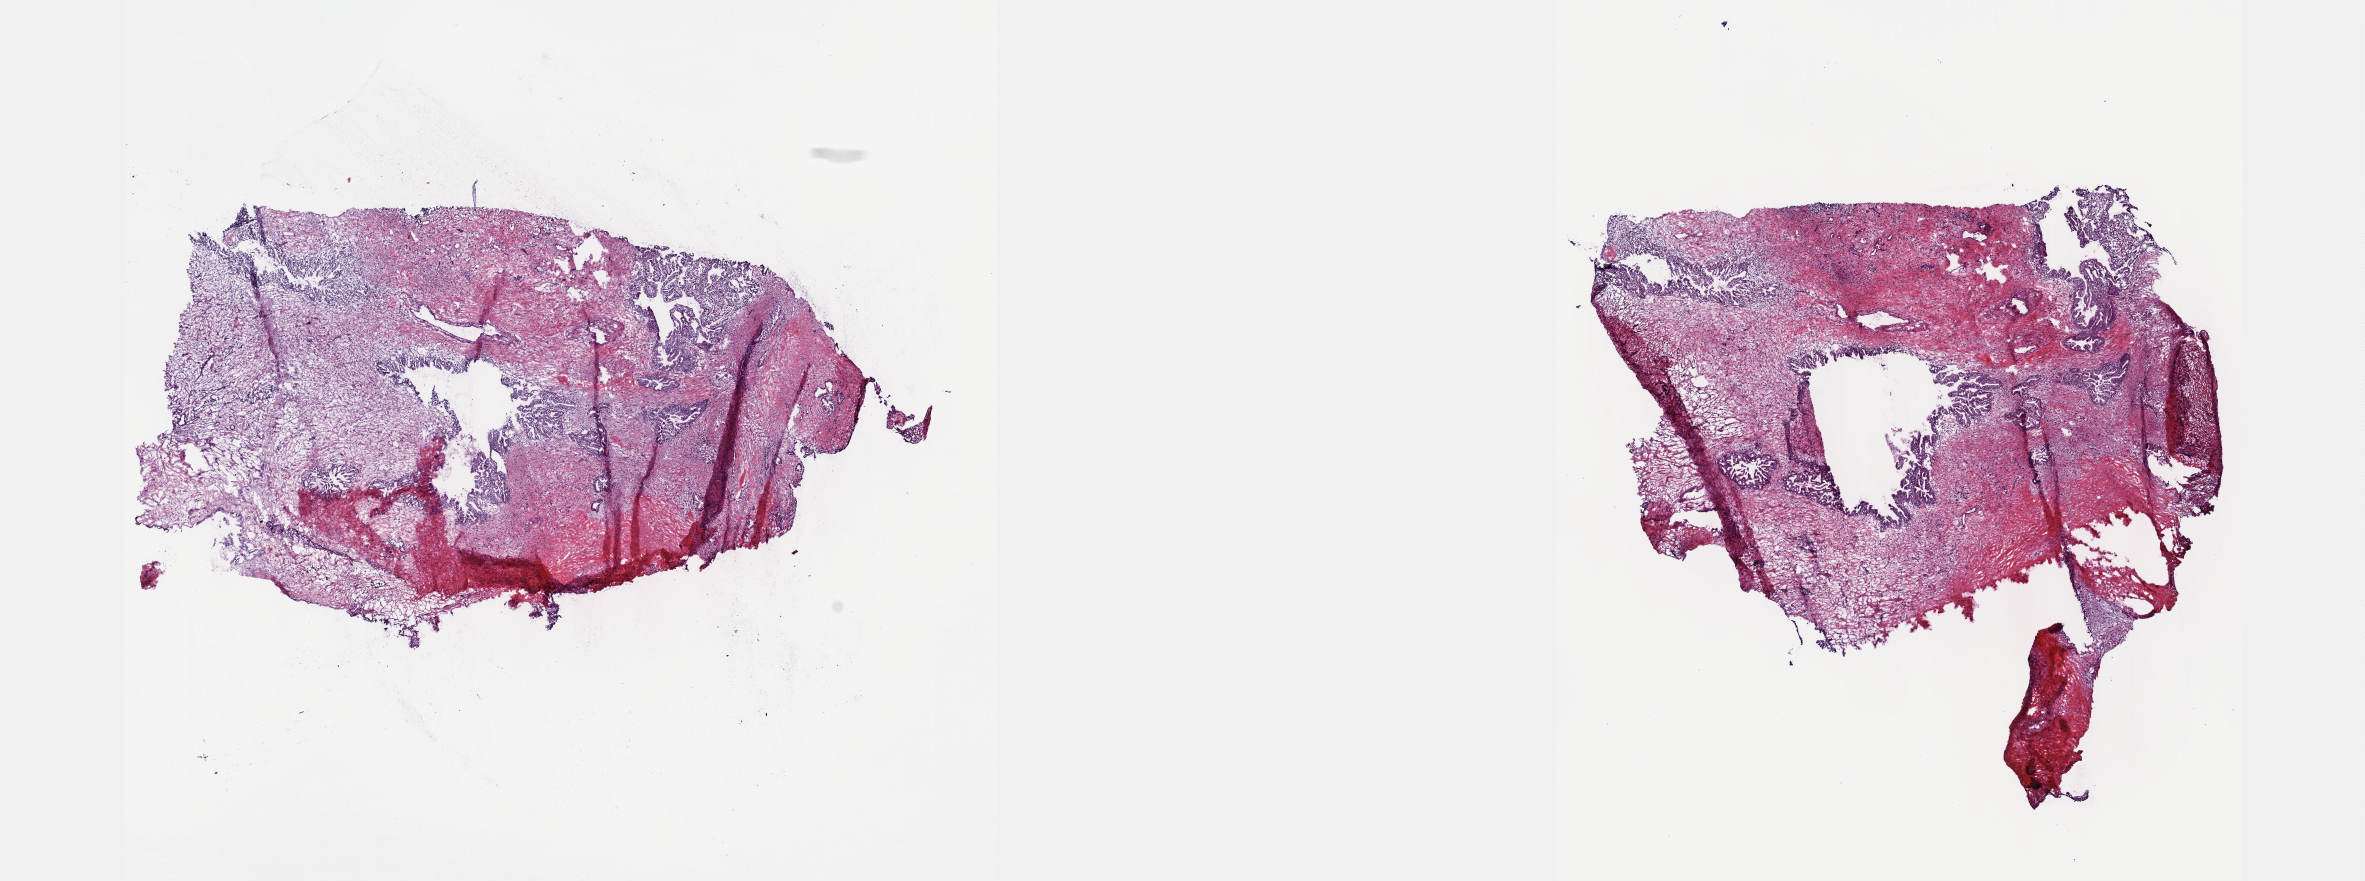
Digitized H&E tissue section (whole slide) — whole scanned area (about 19.1 x 7.1 mm, slide scanned at 40x) shown as a low-resolution overview. Frozen section from the top of the tissue portion. Pancreas, primary tumour sample. Male patient; age at initial diagnosis 67 years. Histologic grade: G3 (poorly differentiated). Composition of this section per pathologist review: tumour cells 30%, tumour nuclei 40%, normal cells 30%, stromal cells 40%, necrosis 0%. Infiltration values recorded for this section: lymphocyte infiltration 0%, monocyte infiltration 0%, neutrophil infiltration 0%.
Histologic diagnosis: Infiltrating duct carcinoma, NOS. Lymph nodes positive (case pathology): 1 of 9 examined. AJCC pathologic stage: IIB (7th edition). TNM: T3 N1 MX.